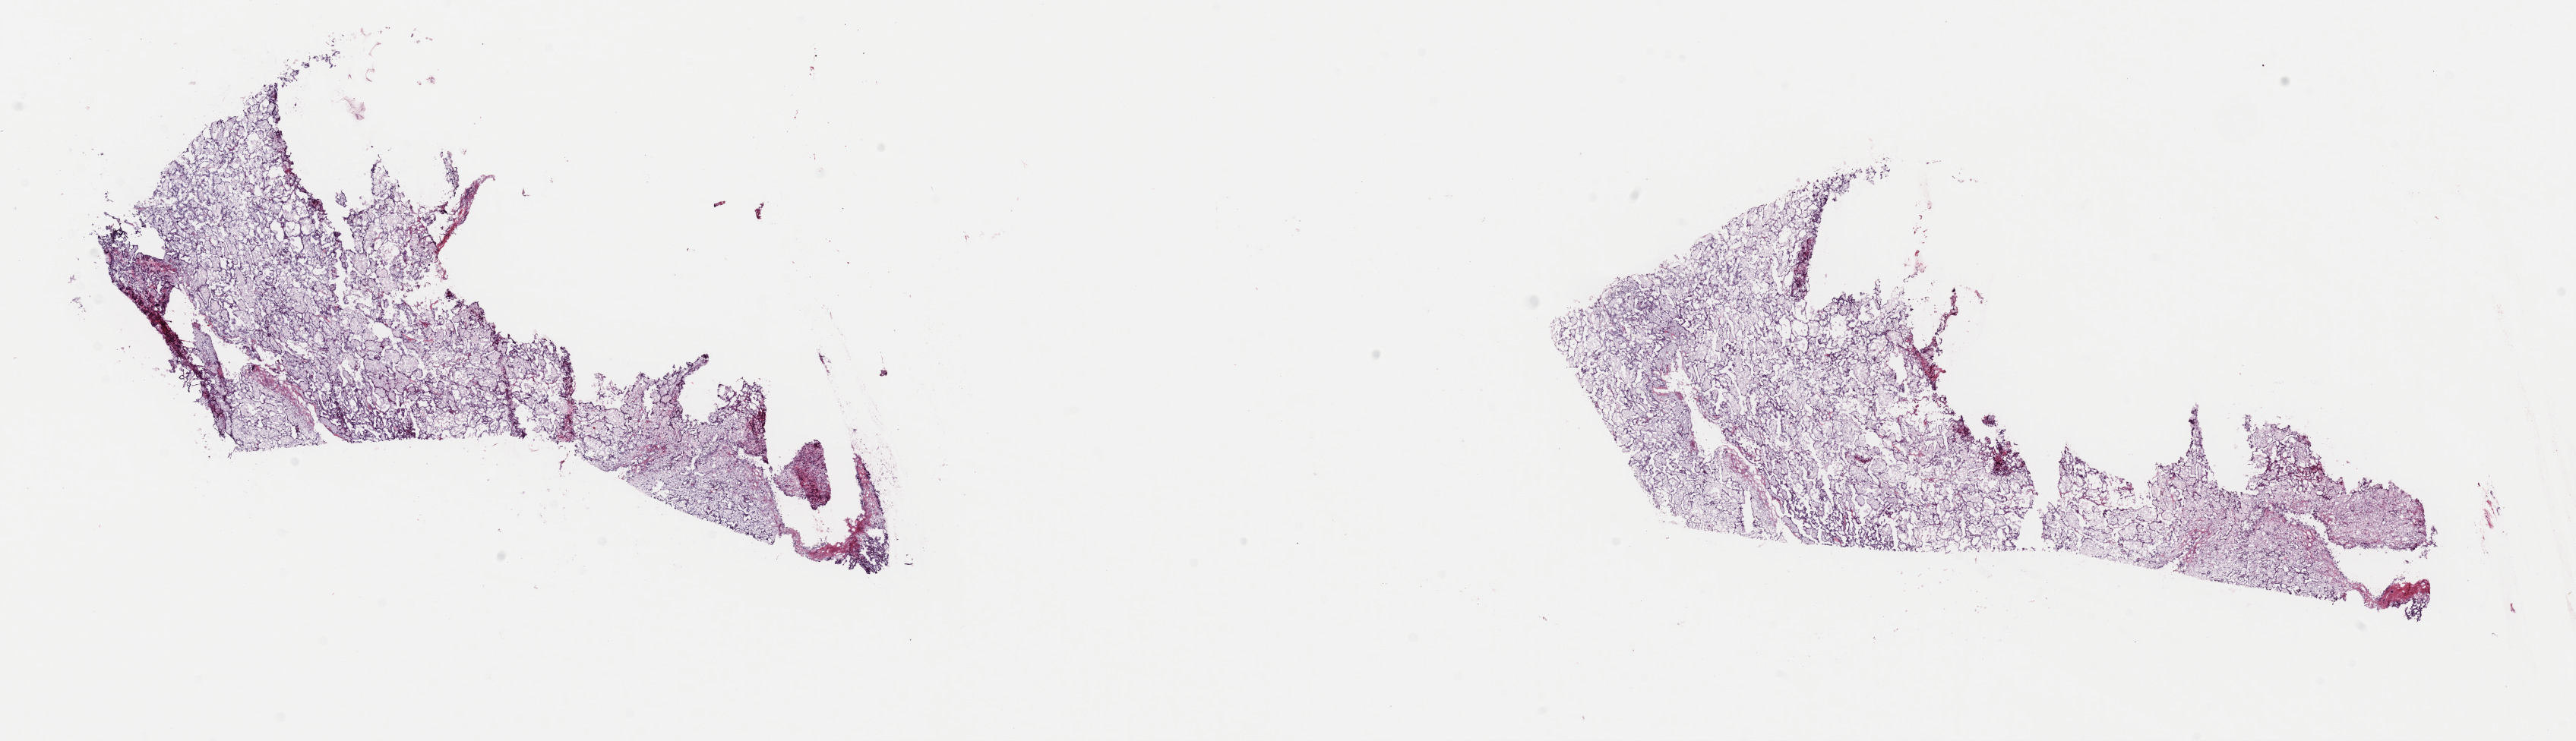
Digitized H&E-stained tissue section (whole slide), whole scanned area (about 26.8 x 7.7 mm) shown as a low-resolution overview; frozen section from the top of the tissue portion; kidney, primary tumour sample. Male patient; age at initial diagnosis 85 years.
Pathologic diagnosis: Papillary adenocarcinoma, NOS.